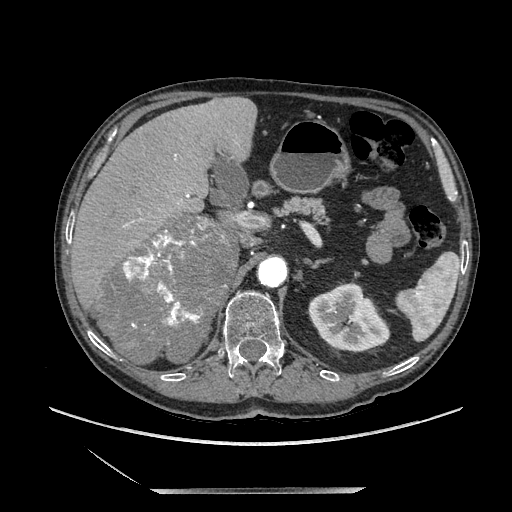
Contrast-enhanced abdominal CT, one axial slice. Slice 129 of 243 in the series (ordered by position). Soft-tissue window (W 400 / L 40 HU). 1.25 mm slice thickness. 512 × 512 image matrix, field of view 420 × 420 mm. Male patient. From the clinical record (not read from this slice): diagnosis: adrenocortical carcinoma; tumour side: right adrenal; tumour size at pathology: 16 cm; Ki-67 index: 17 %; stage (as recorded): 3.
Outlined on this slice (semi-automatic segmentation, software-assisted and operator-edited):
- mass: bounding box <100,217,236,365> (left, top, right, bottom; pixels)